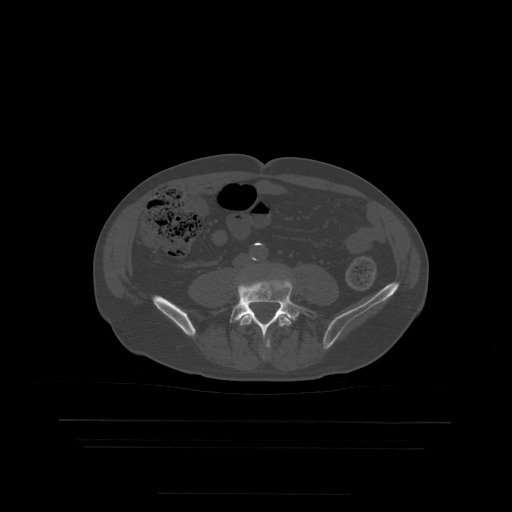
CT including the spine, one axial slice; bone window (W 1800 / L 400 HU); 512 × 512 image matrix, field of view 436 × 436 mm. Patient age 68 years. Case-level facts recorded for this patient, not image findings: primary cancer: urothelial.
Structures marked on this image (semi-automatically segmented with operator editing):
- L4 vertebra: box from (x=240, y=315) to (x=292, y=349) px
- L5 vertebra: (x=217, y=281)–(x=318, y=350)